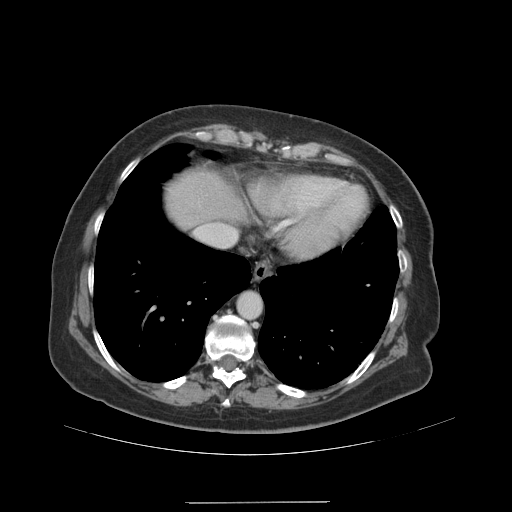
Contrast-enhanced abdominal CT (liver protocol), one axial slice. Position 87 of 99 along the scan axis. Reconstruction kernel STANDARD. 140 kVp. Soft-tissue window (W 400 / L 40 HU). 2.5 mm slice thickness. 512 × 512 image matrix, field of view 440 × 440 mm. From the clinical record (not read from this slice): diagnosis: hepatocellular carcinoma (patient treated with transarterial chemoembolisation; whether this scan precedes or follows treatment is not stated here); TNM stage (as recorded): Stage-IVA; Child-Pugh class: A.
Outlined on this slice (semi-automatic segmentation, software-assisted and operator-edited):
- abdominal aorta: box from (x=238, y=293) to (x=260, y=317) px
- liver parenchyma outside the tumour (the mass and vessels are separate outlines, so this box may not span the whole liver): (x=166, y=172)–(x=244, y=228)